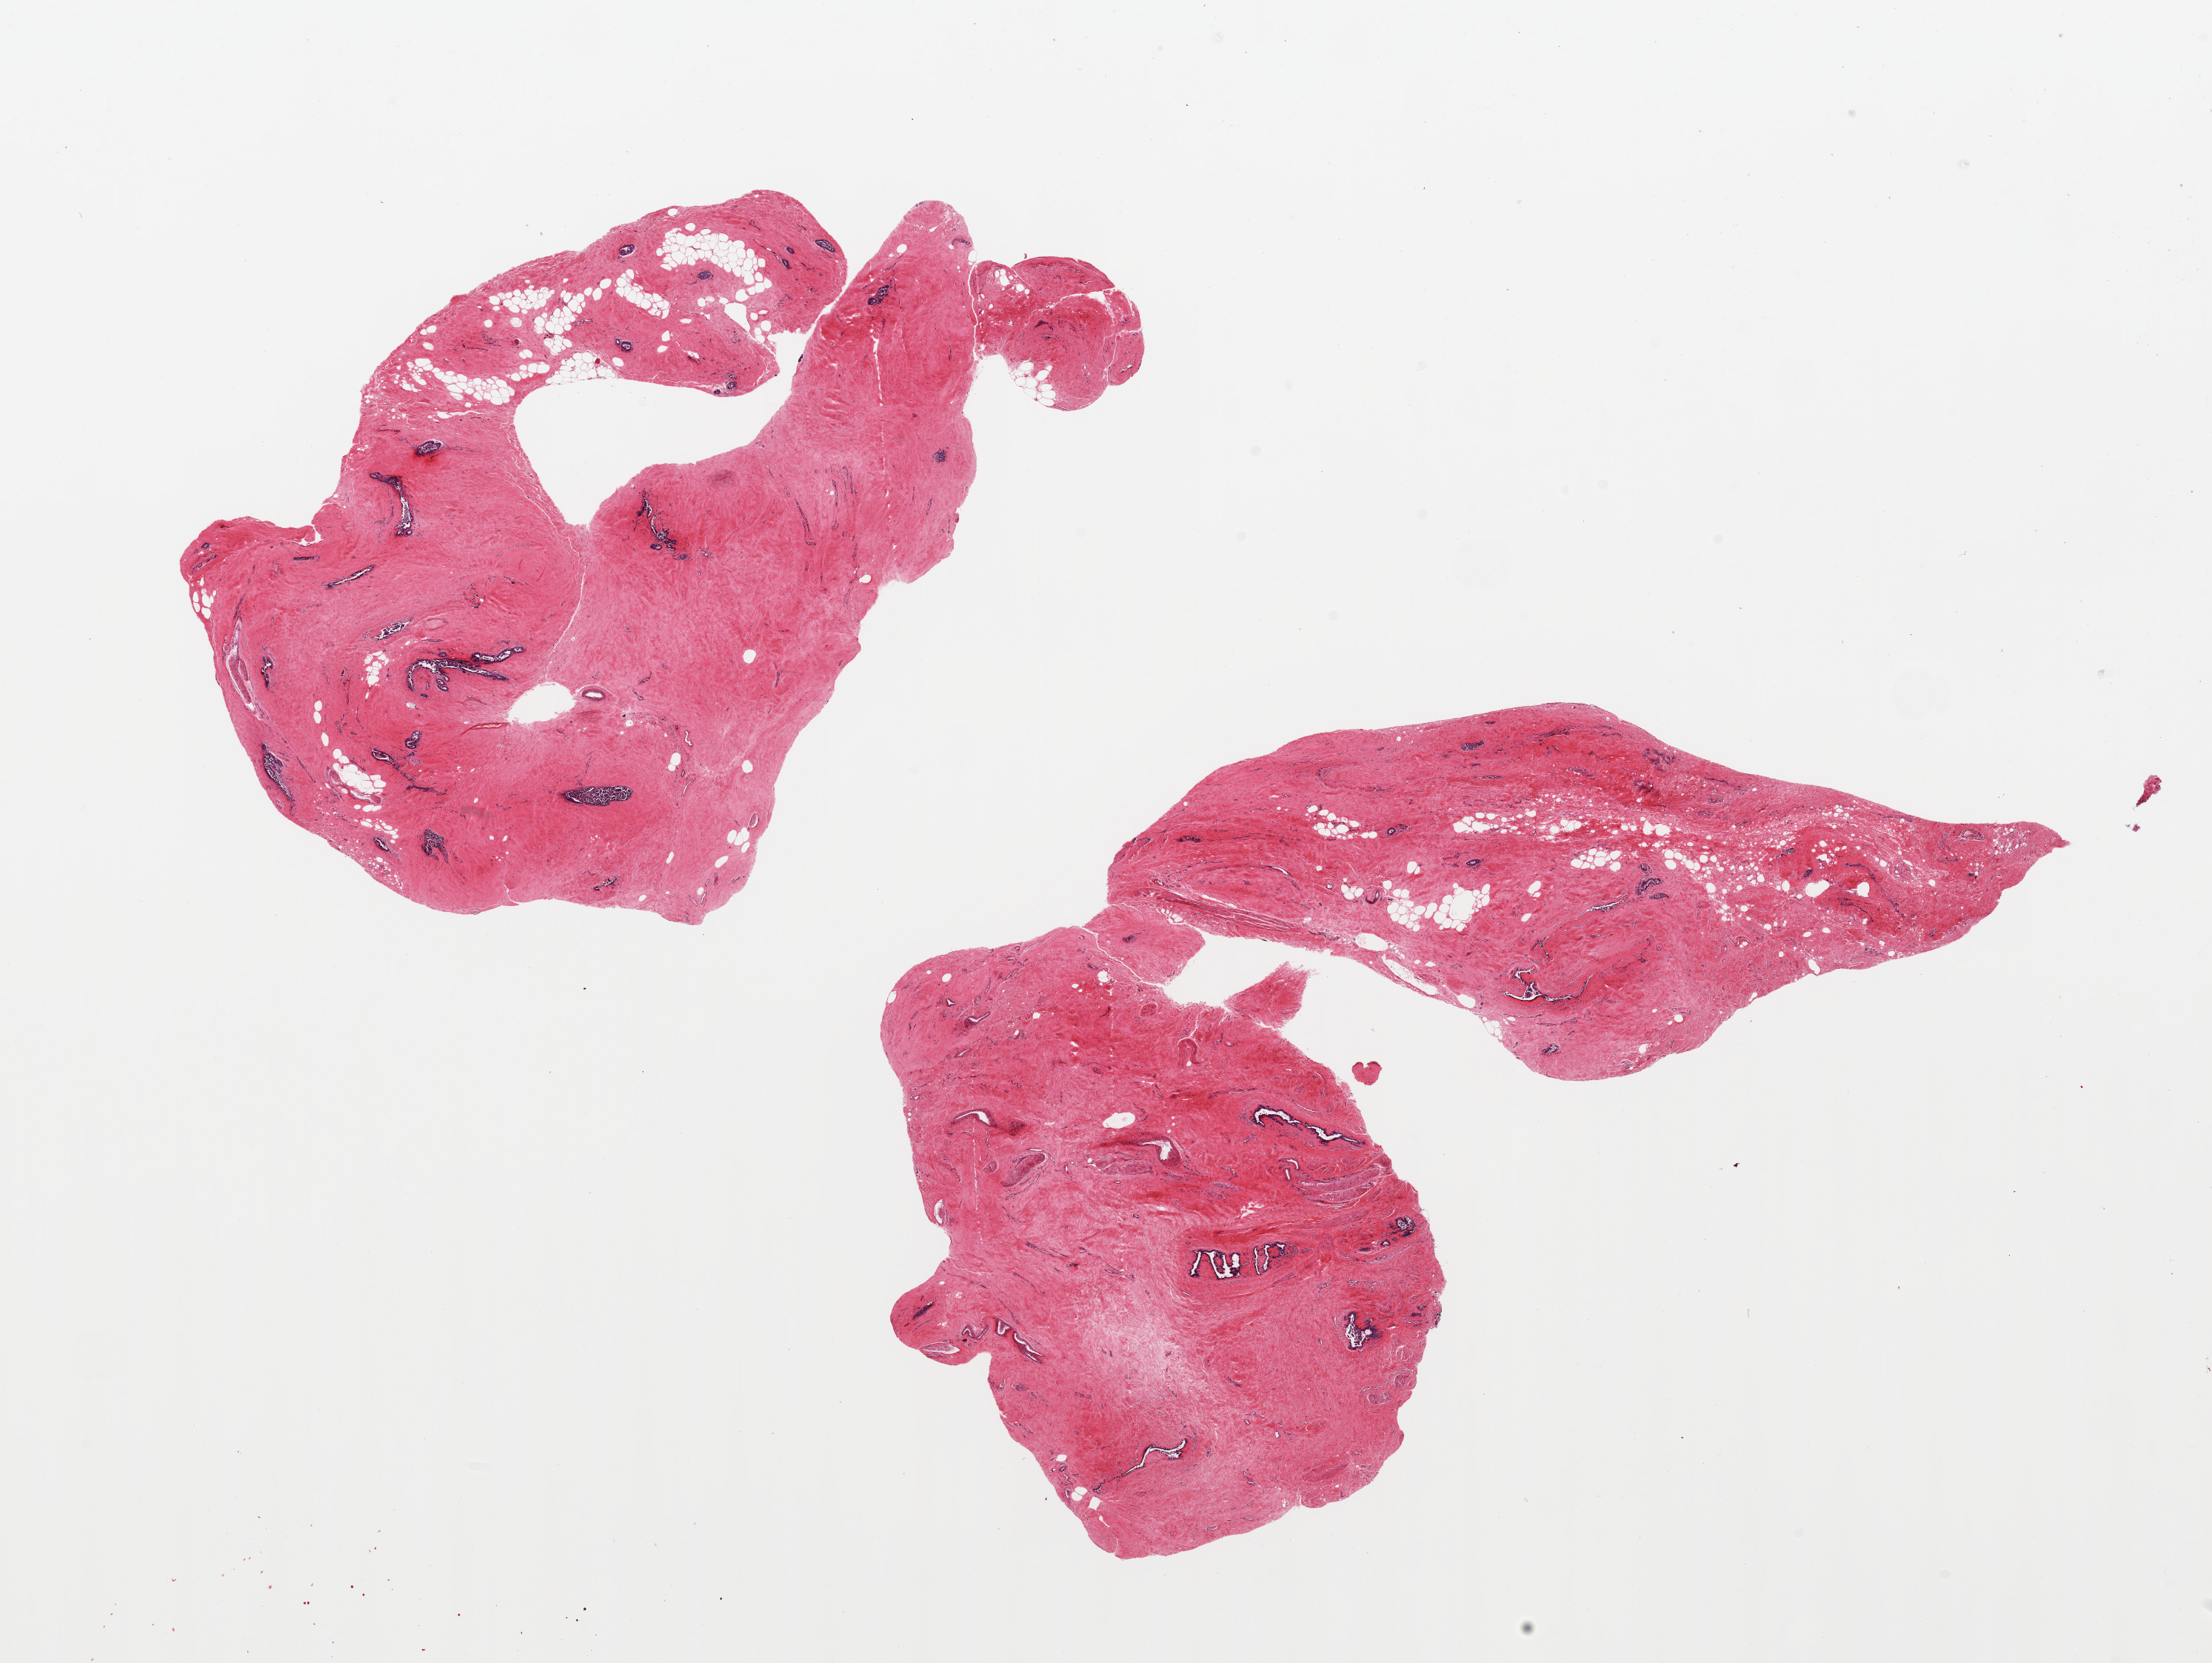
Digitized hematoxylin and eosin (H&E)-stained section, brightfield — whole scanned area (about 23.6 x 17.8 mm, slide scanned at 20x) shown as a low-resolution overview, PAXgene-fixed, paraffin-embedded tissue, section of breast (target tissue), tissue donor sample. Donor: male.
Reviewer comment on this tissue sample: 2 pieces; ductal and stromal gynecomastoid hyperplasia.